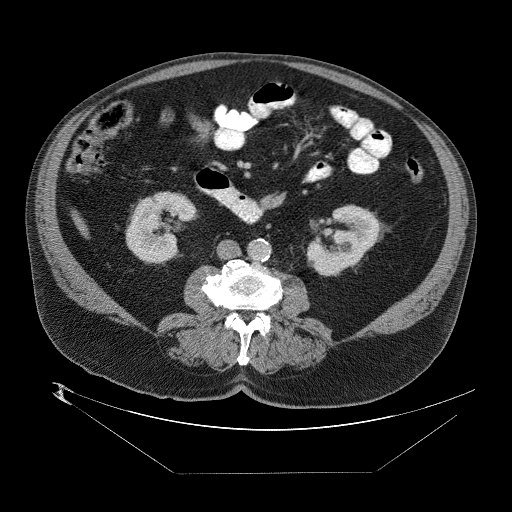
Contrast-enhanced abdominal CT (liver protocol), one axial slice. Position 2 of 89 along the scan axis. 140 kVp. One of 2 acquisitions stored at this slice position. Soft-tissue window (W 400 / L 40 HU). 2.5 mm slice thickness. 512 × 512 image matrix. From the clinical record (not read from this slice): diagnosis: hepatocellular carcinoma (patient treated with transarterial chemoembolisation; whether this scan precedes or follows treatment is not stated here); TNM stage (as recorded): Stage-II.
Outlined on this slice (semi-automatically segmented with operator editing):
- abdominal aorta: bounding box [x1, y1, x2, y2] px = [249, 239, 271, 263]
- liver parenchyma outside the tumour (the mass and vessels are separate outlines, so this box may not span the whole liver): [72, 212, 86, 232]